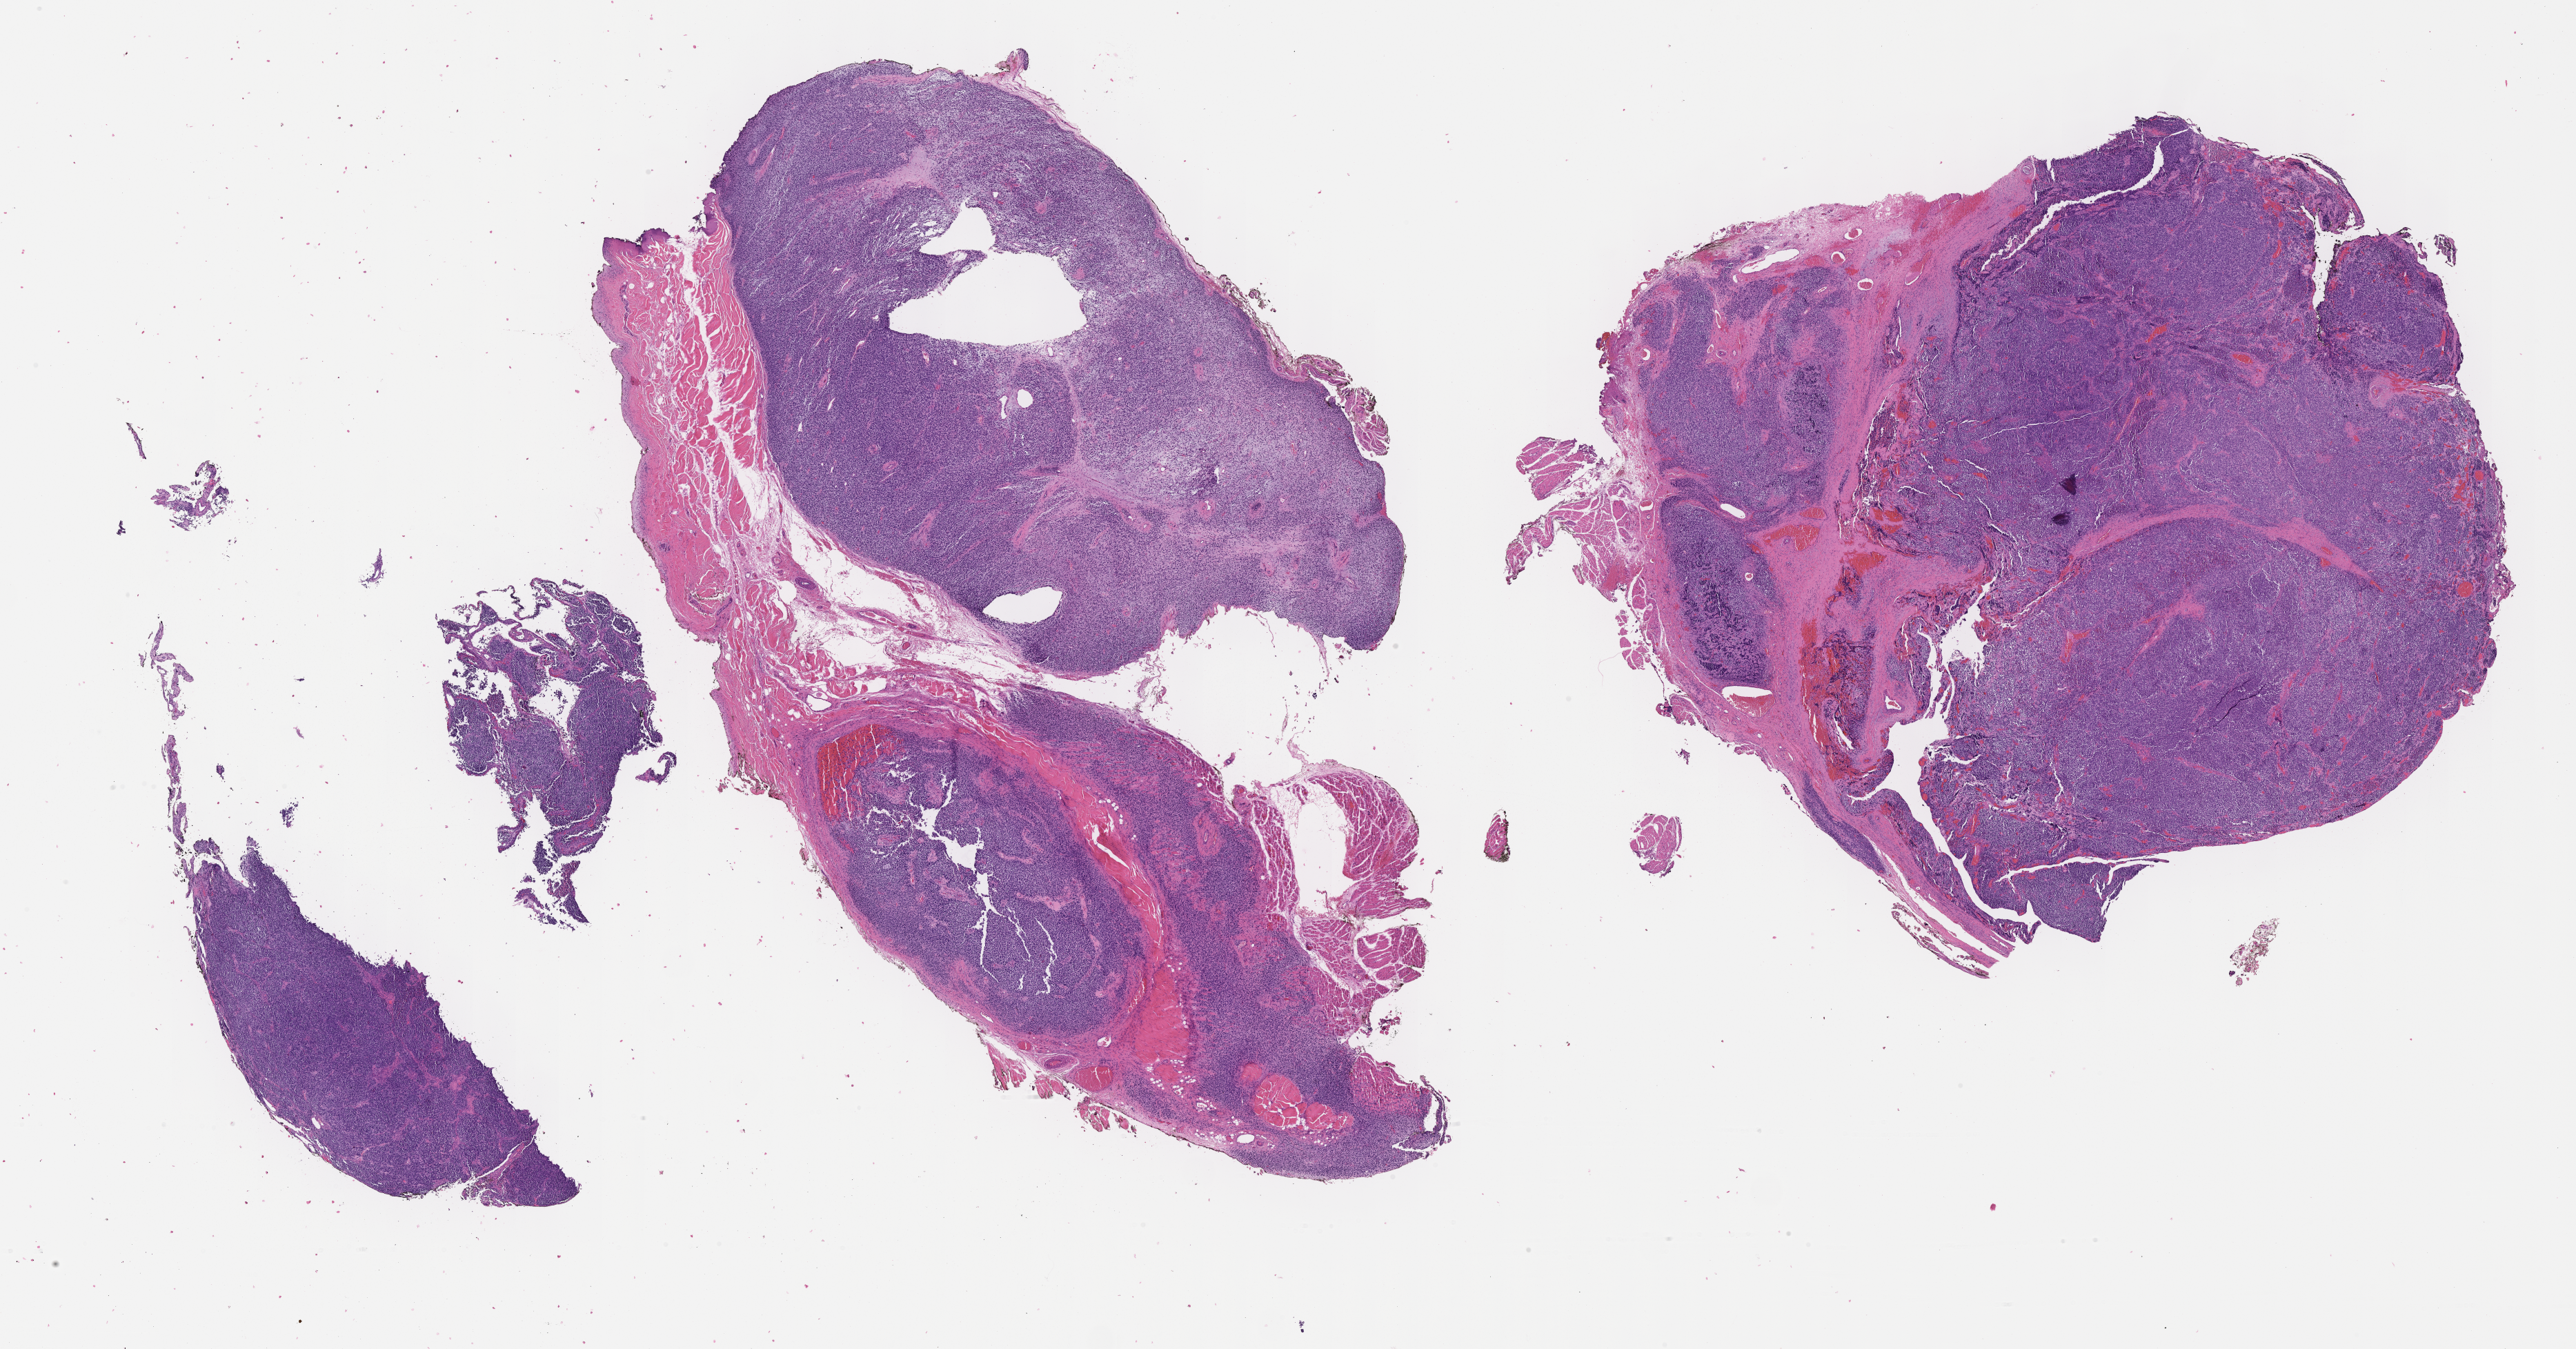
Digitized H&E-stained section of tumor tissue, a low-resolution overview of the entire scanned area, about 30.2 x 15.8 mm, formalin-fixed paraffin-embedded section. Female patient, age at diagnosis 11.4 years.
• stage (as recorded): 2
• diagnosis: rhabdomyosarcoma; histological classification: embryonal rhabdomyosarcoma
• metastatic status at presentation (as recorded): non-metastatic